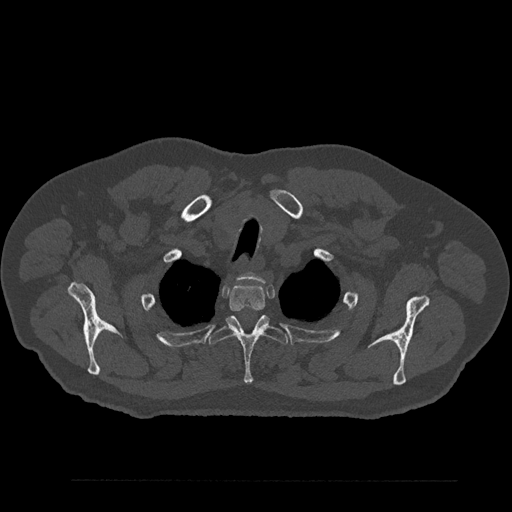
CT including the spine, one axial slice. Slice 701 of 797 in the series (ordered by position). 120 kVp. Bone window (W 1800 / L 400 HU). 0.5 mm slice thickness. 512 × 512 image matrix, field of view 430 × 430 mm. Male patient, age 61 years. From the clinical record (not read from this slice): primary cancer: prostate.
Annotated regions visible in this slice (semi-automatically segmented with operator editing):
- T1 vertebra: bounding box <238,272,264,282> (left, top, right, bottom; pixels)
- T2 vertebra: <228,283,266,312>
- T3 vertebra: <208,315,288,384>